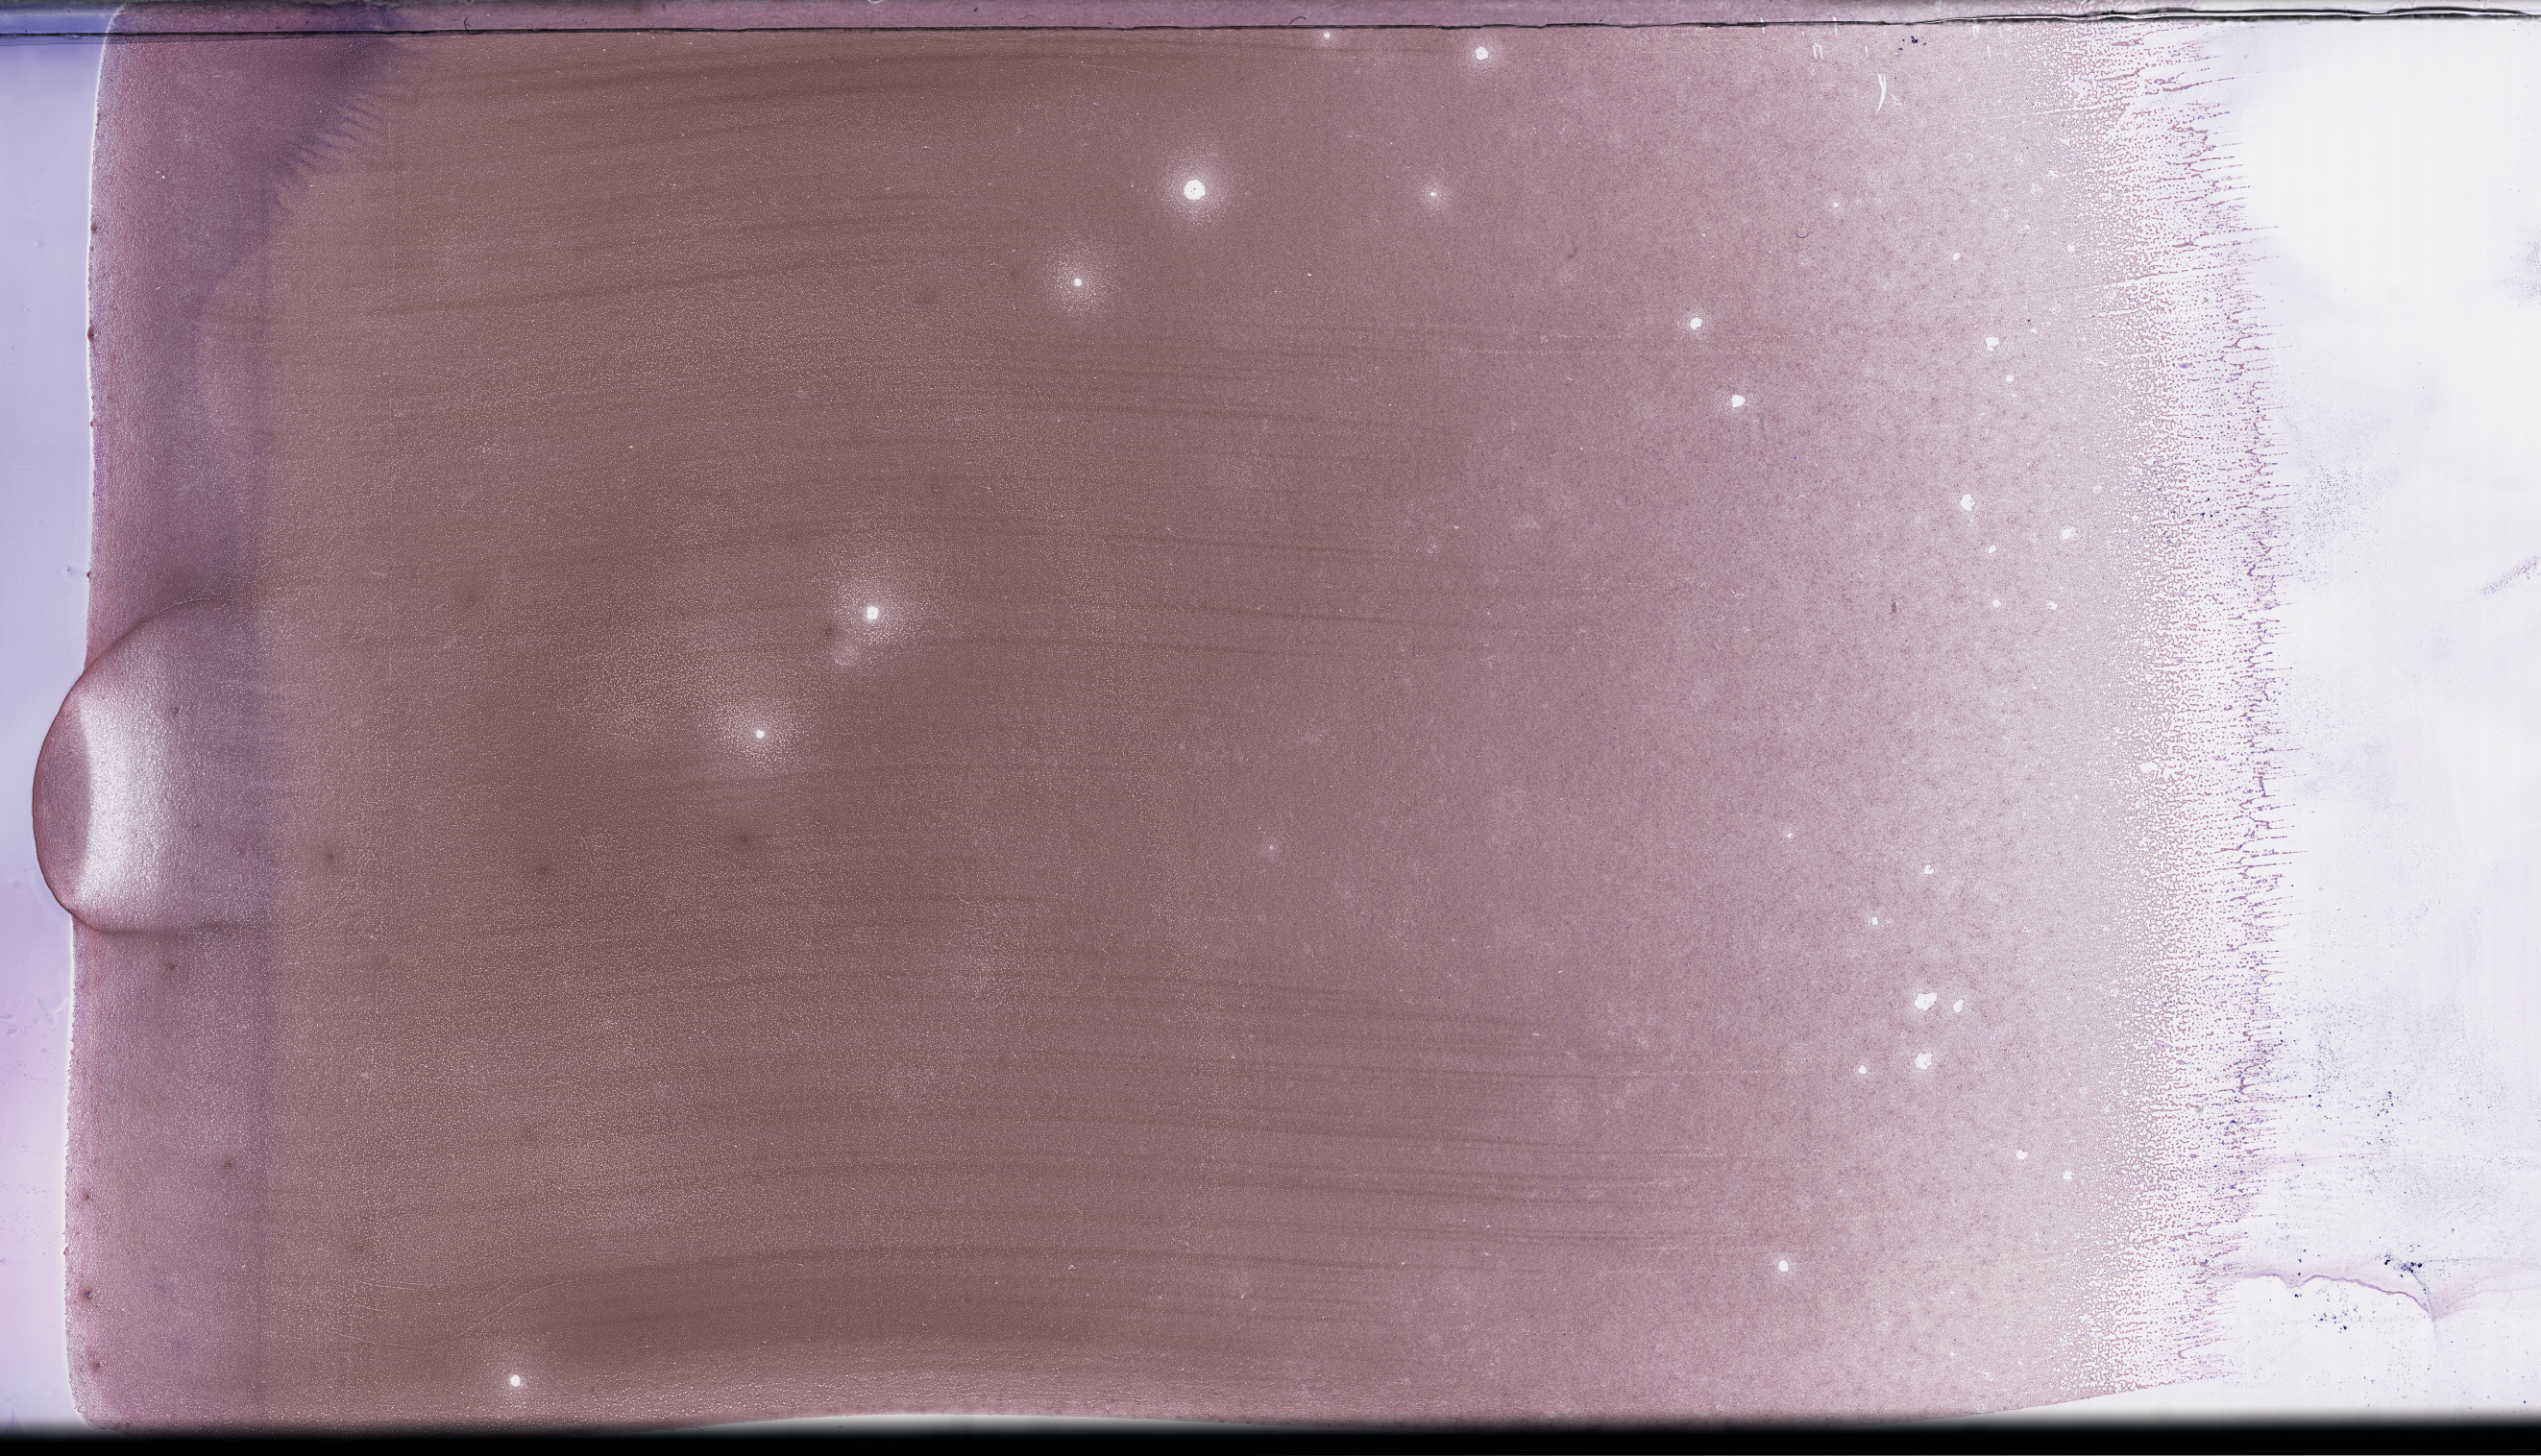
Whole-slide image of a bone marrow smear, Wright-Giemsa stain, a low-resolution overview of the entire scanned area, about 42.7 x 24.5 mm, smear from an EDTA sample, specimen time point: collected at baseline (before treatment). Male patient.
- from a patient with: Plasma Cell Myeloma